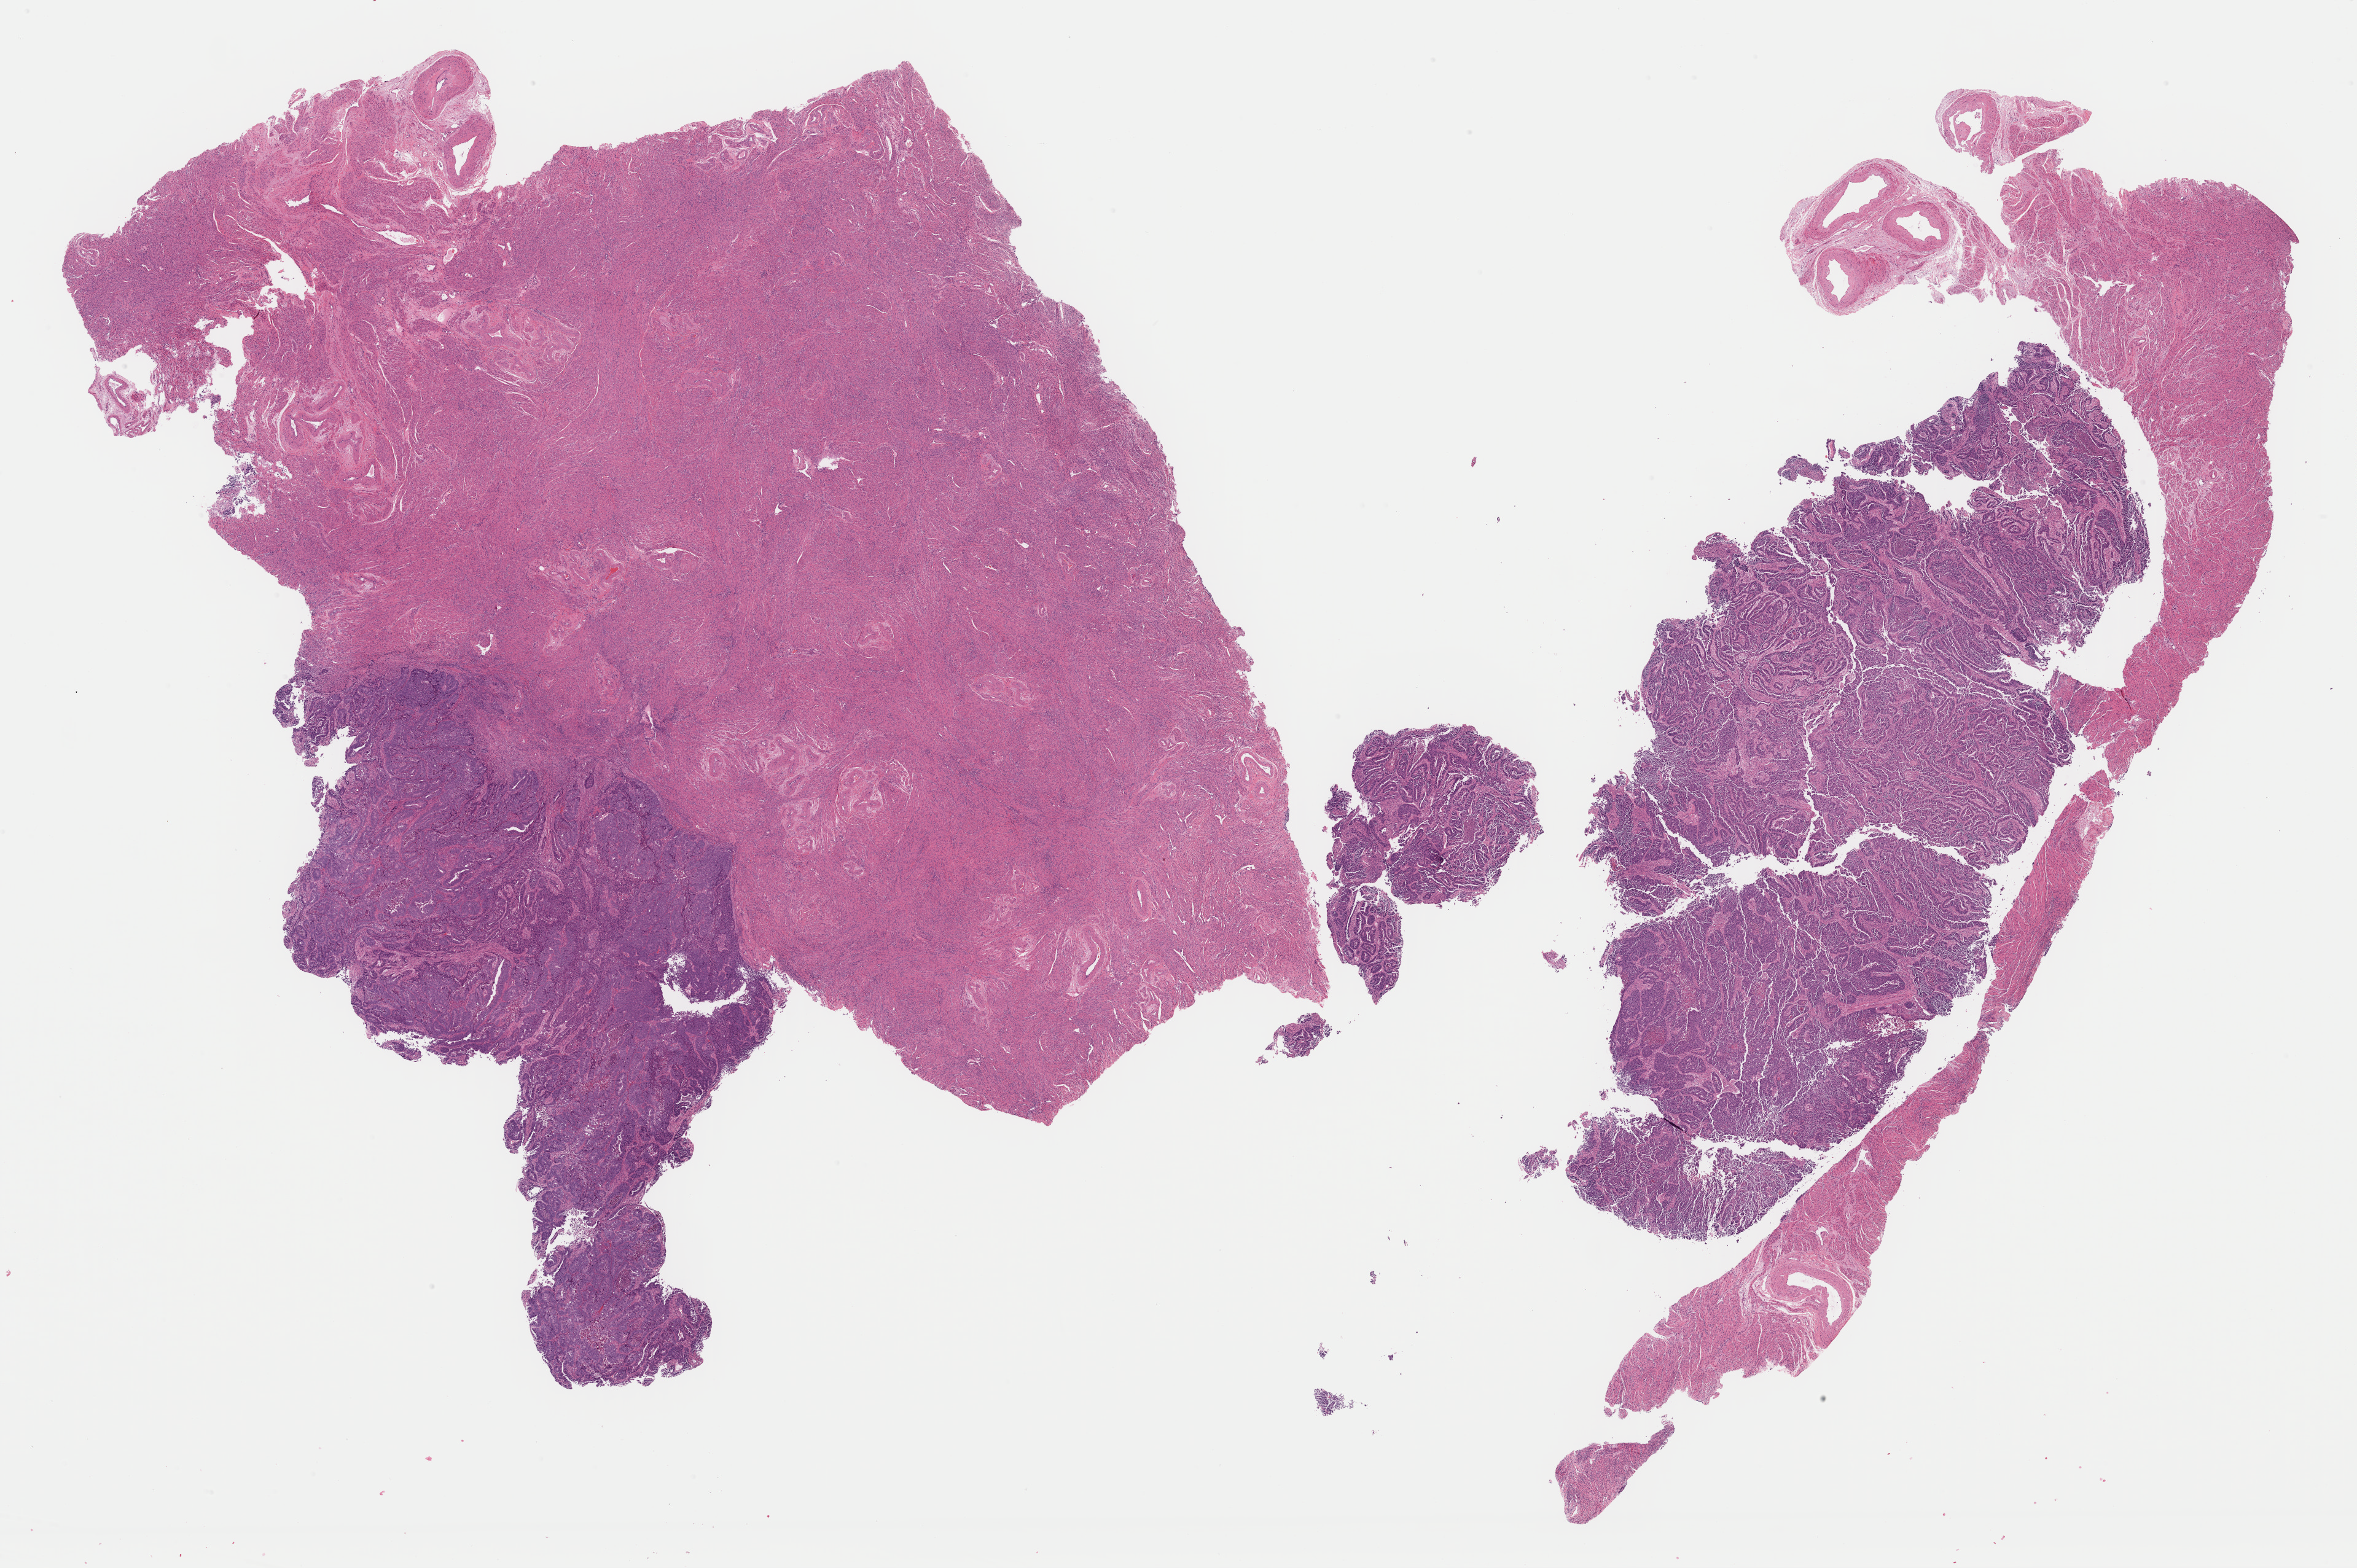
Whole-slide histology image, Hematoxylin and eosin (H&E) stained, whole scanned area (about 30.3 x 20.2 mm, acquisition: 40x scan) shown as a low-resolution overview, FFPE section, uterus, primary tumour sample. Patient: female, age at initial diagnosis 71 years. Histologic grade: G3 (poorly differentiated).
Pathologic diagnosis: Endometrioid adenocarcinoma, NOS (endometrium). FIGO stage: IA.